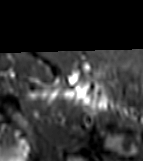
MRI of an extremity soft-tissue mass, one axial slice; position 55 of 81 along the scan axis; STIR; MR volume resampled by the dataset authors to the PET/CT grid (not the native acquisition matrix); 3.27 mm slice thickness; 143 × 161 image matrix. Female patient. From the clinical record (not read from this slice): histological type: myxofibrosarcoma; grade: intermediate; site of the primary tumour: left thigh.
Outlined on this slice (expert contour drawn on MRI and transferred to this co-registered scan by the dataset authors):
- gross tumour volume including surrounding oedema: bounding box (x1, y1, x2, y2) in pixels: (33, 79, 114, 107)